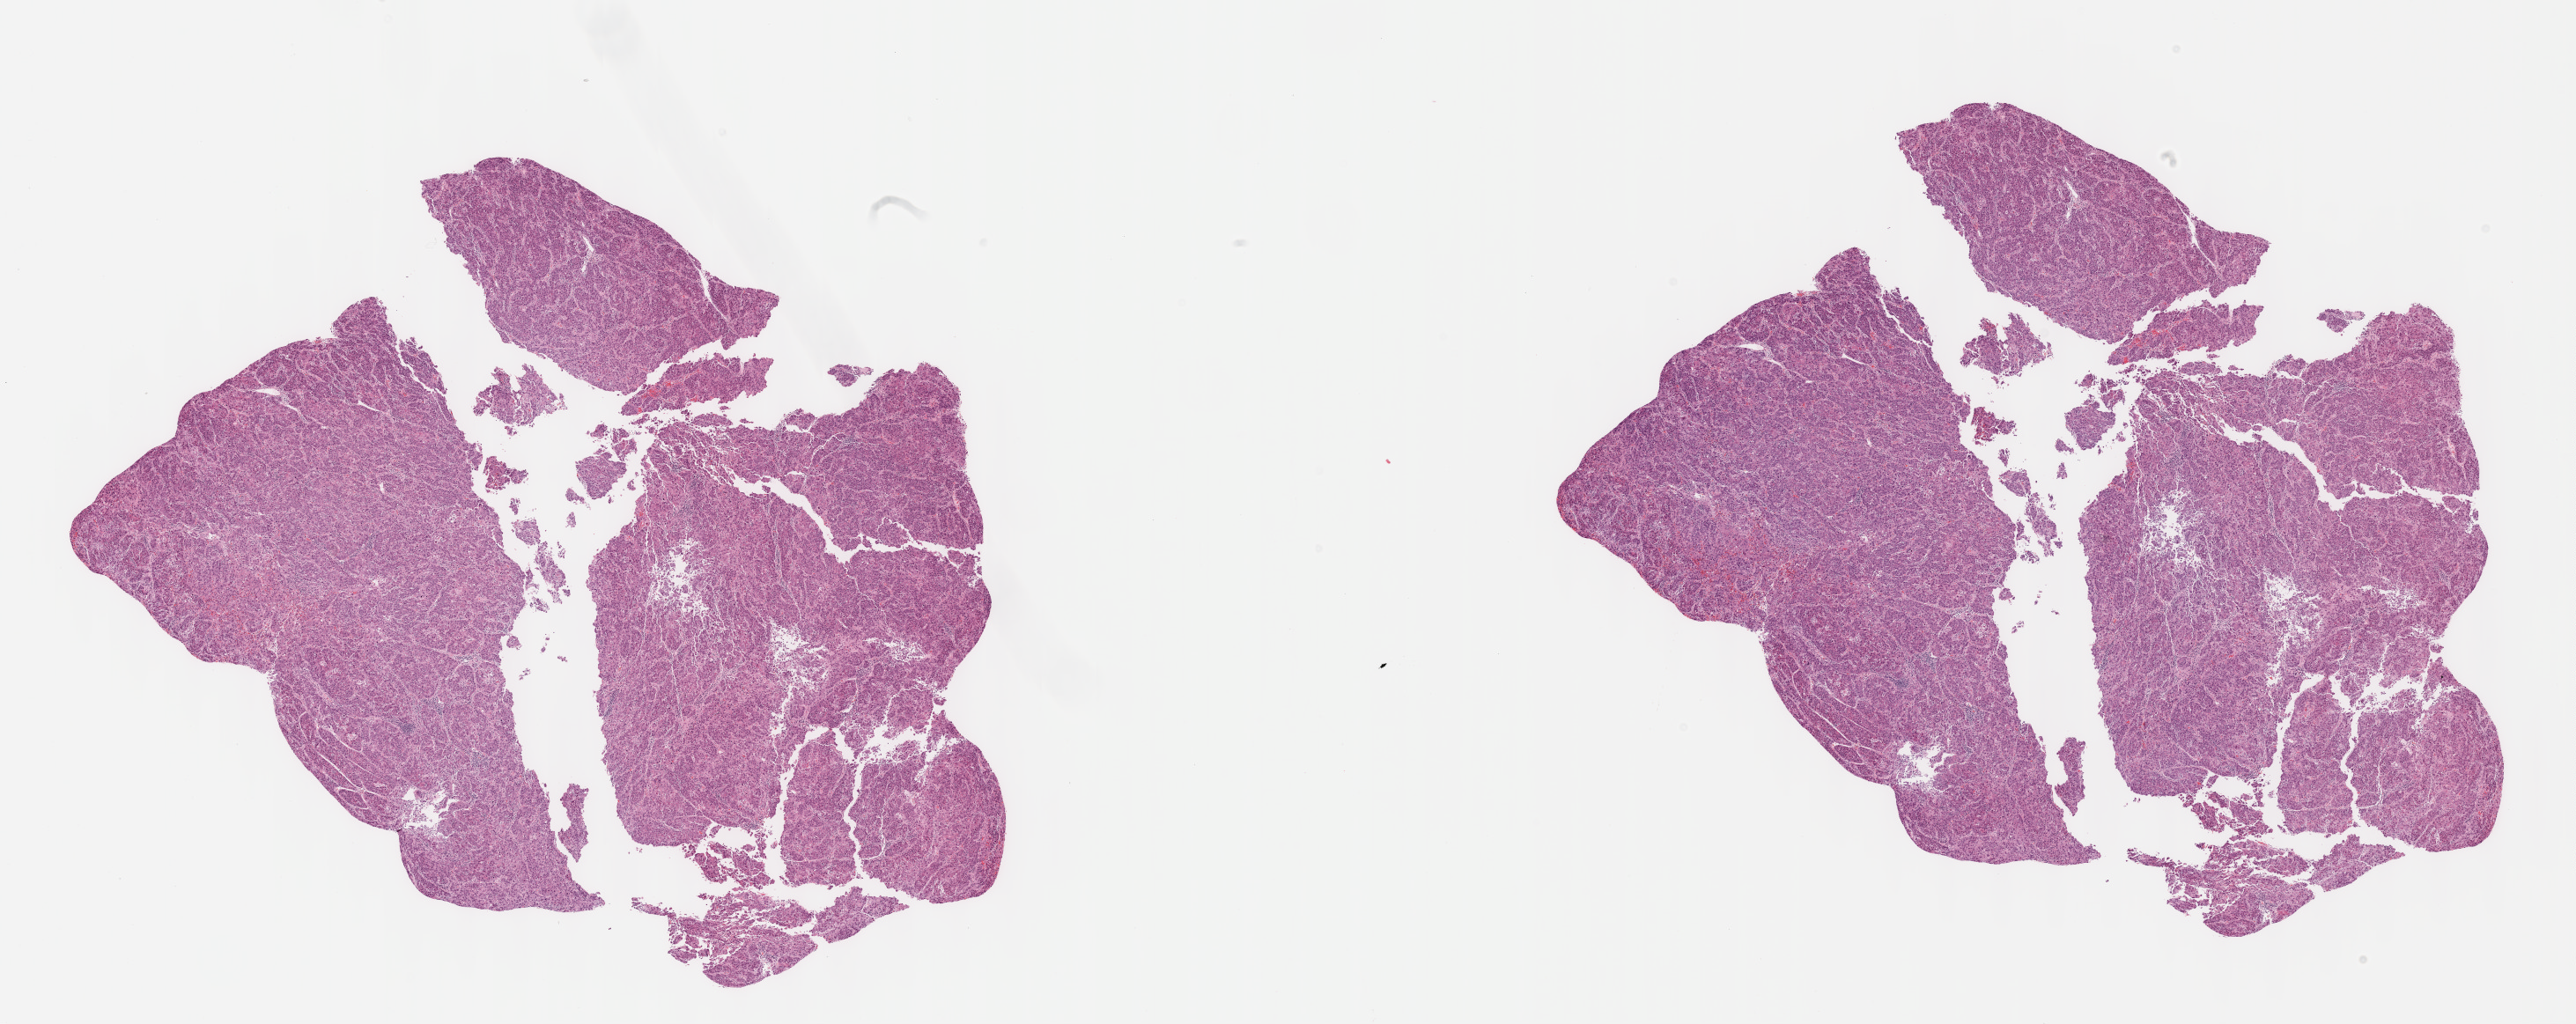
H&E whole-slide image, whole scanned area (about 23.6 x 9.4 mm) shown as a low-resolution overview. FFPE section. Liver, primary tumour sample. Male, age 59 years at initial diagnosis. Histologic grade: G4 (undifferentiated).
AJCC pathologic stage: I (7th edition). TNM: T1 NX MX. Pathologic diagnosis: Hepatocellular carcinoma, NOS.